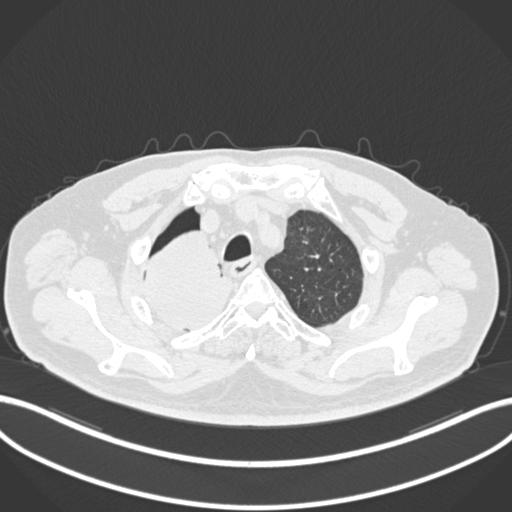
Chest CT, one axial slice. Slice 177 of 218 in the series (ordered by position). 120 kVp. Lung window (W 1500 / L -600 HU). 1 mm slice thickness. 512 × 512 image matrix, field of view 400 × 400 mm. Male patient, age 68 years. From the clinical record (not read from this slice): clinical TNM (as recorded): T2a N0 M0.
Annotated regions visible in this slice (bounding box drawn by a radiologist):
- lung tumour (recorded histology: adenocarcinoma): bounding box (x1, y1, x2, y2) in pixels: (141, 227, 232, 337)